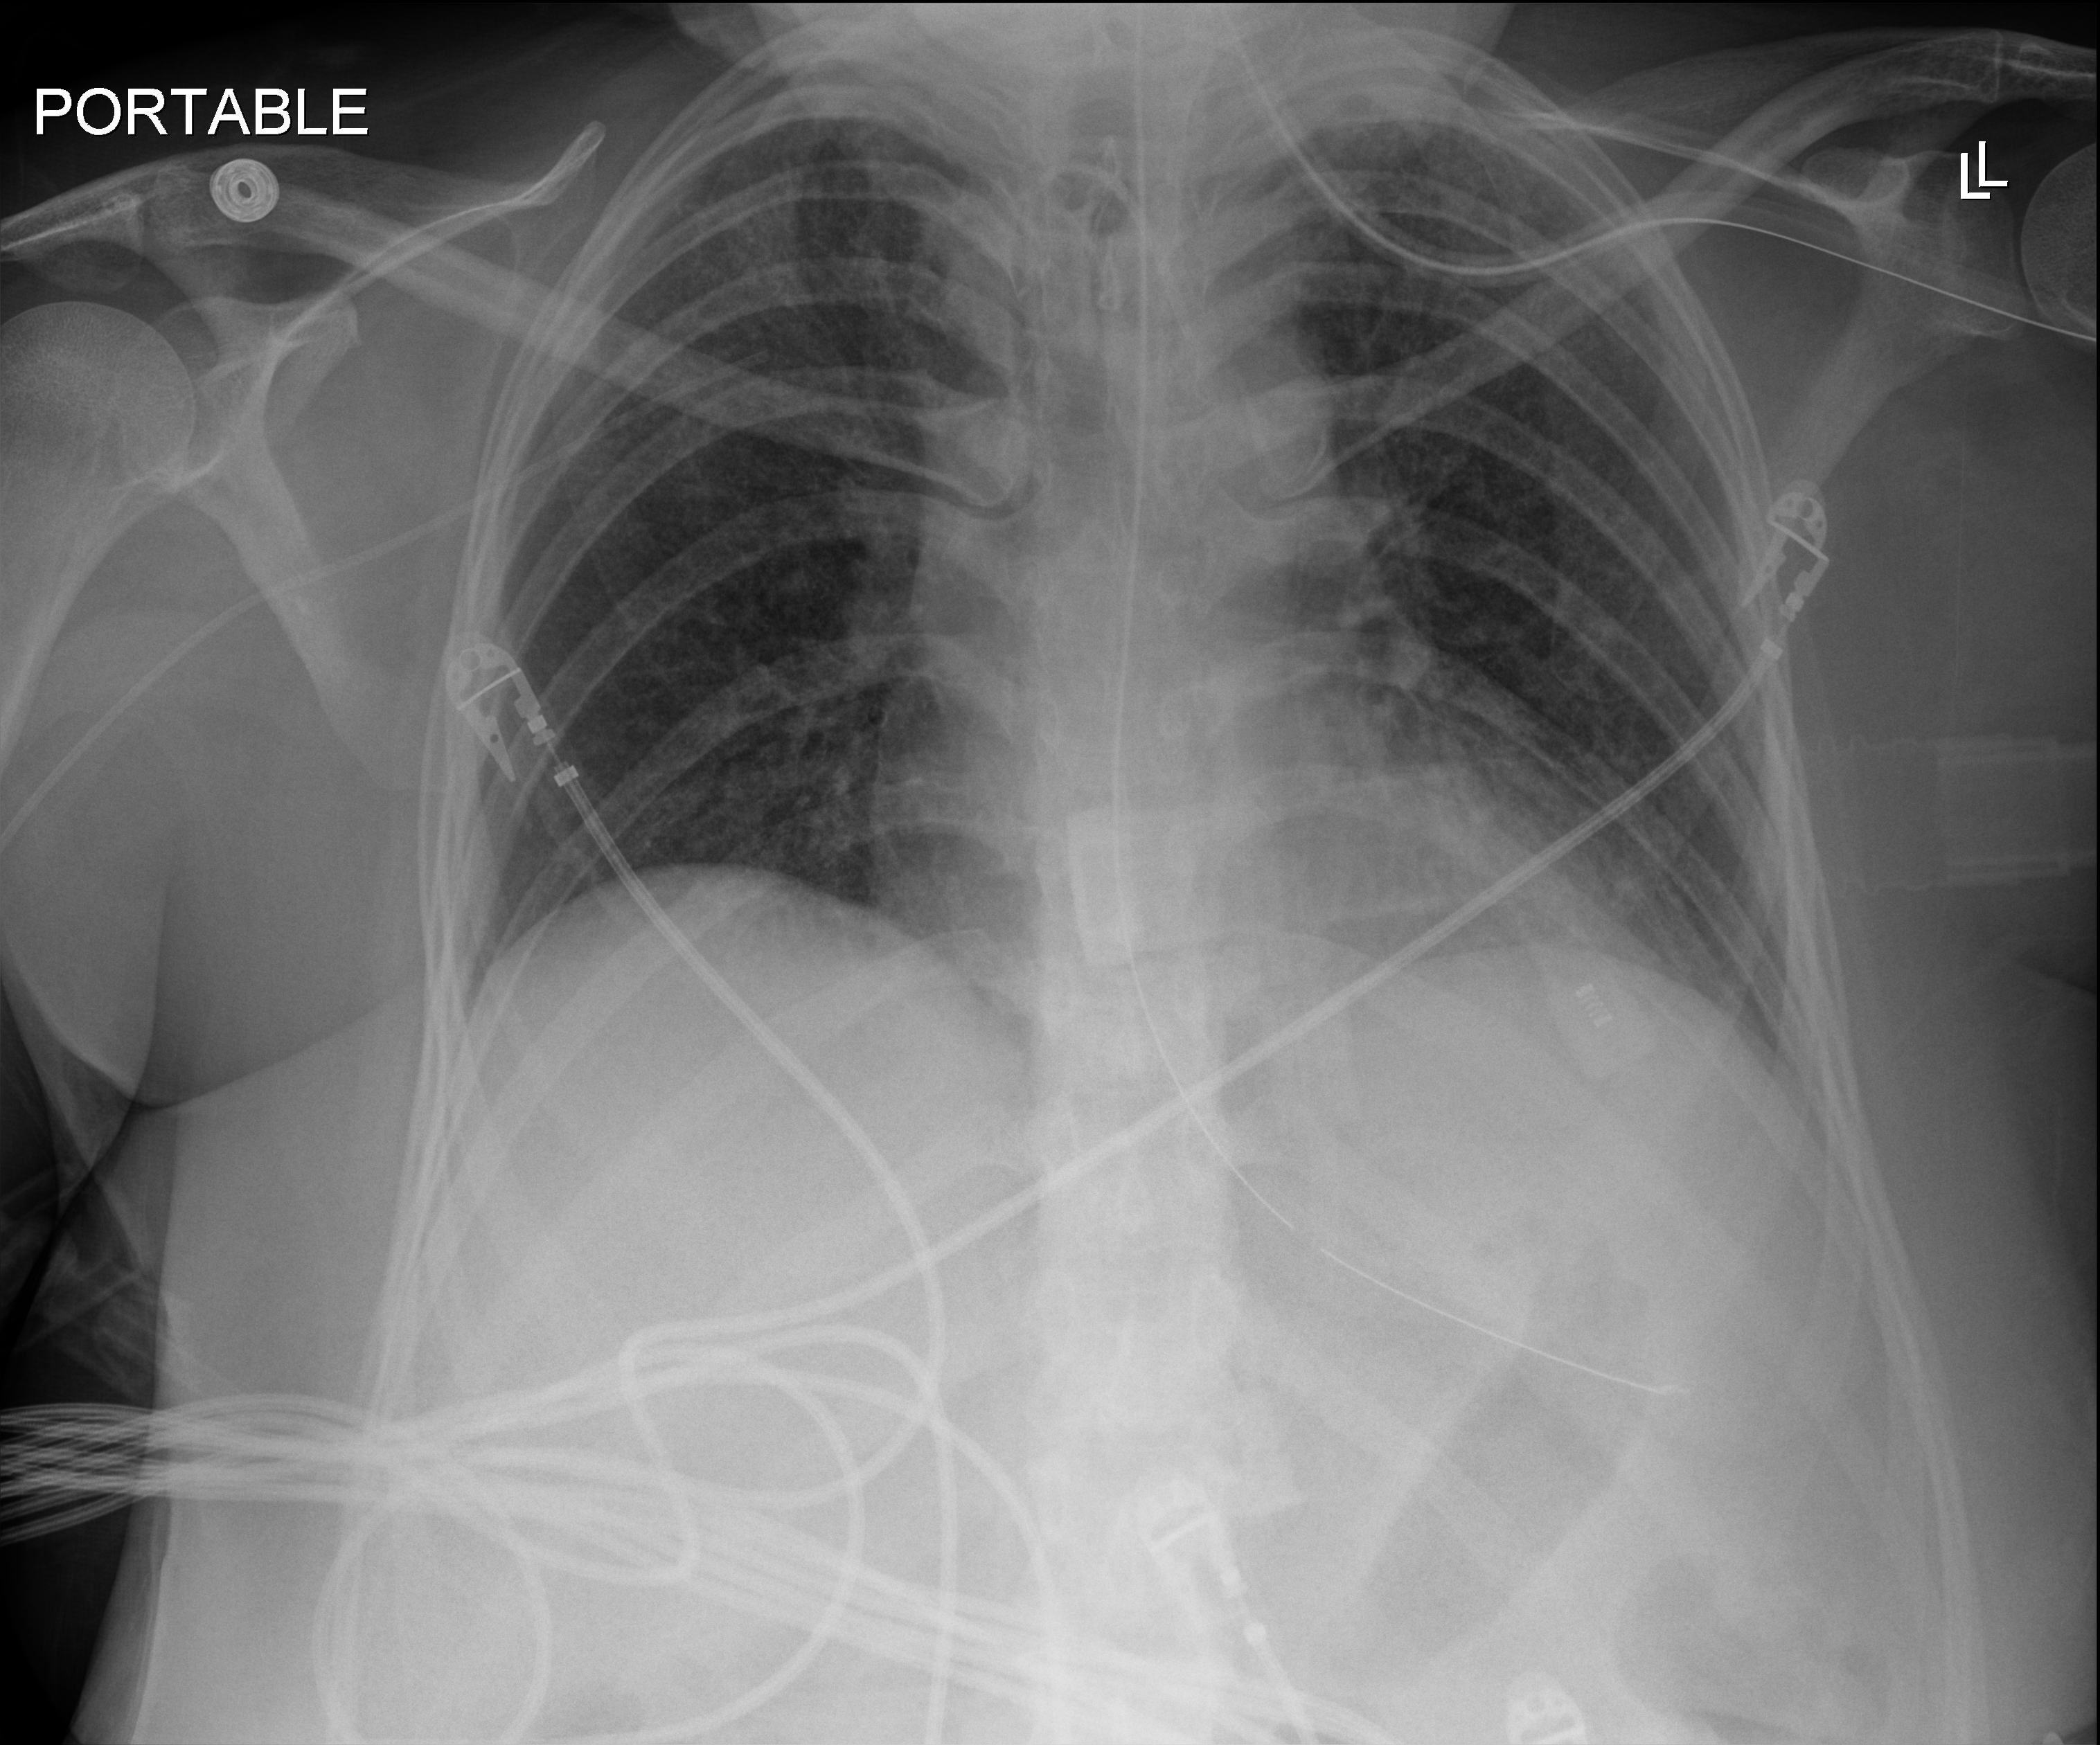
Chest radiograph, anteroposterior (AP) projection. Patient hospitalised with COVID-19; female, aged 18–59 years.
Hospital-stay facts (about this admission, not read from this image; timing relative to this image not recorded): mechanically ventilated during this hospital stay: yes; admitted to intensive care during this hospital stay: yes.